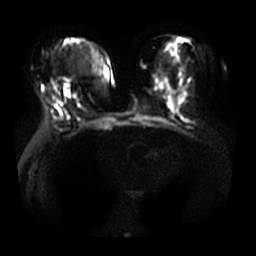
Breast MRI, one axial slice. Slice 14 of 33 in the series (ordered by position). Diffusion-weighted series; image 2 of 4 stored at this slice position (different b-values; order by instance number). 3 T. 256 × 256 image matrix, field of view 360 × 360 mm. Female patient.
Annotated regions visible in this slice (expert manual segmentation):
- tumour on diffusion-weighted imaging: bounding box [x1, y1, x2, y2] px = [64, 79, 70, 86]